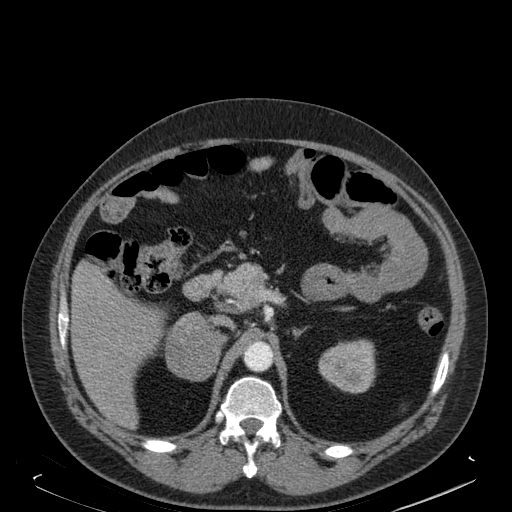
Contrast-enhanced abdominal CT, one axial slice. Position 111 of 181 along the scan axis. Soft-tissue window (W 400 / L 40 HU). 512 × 512 image matrix. Male patient. From the clinical record (not read from this slice): diagnosis: adrenocortical carcinoma; tumour side: right adrenal; tumour size at pathology: 7.5 cm; Ki-67 index: 25 %; stage (as recorded): 4.
Annotated regions visible in this slice (semi-automatically segmented with operator editing):
- mass: bounding box <165,312,217,378> (left, top, right, bottom; pixels)